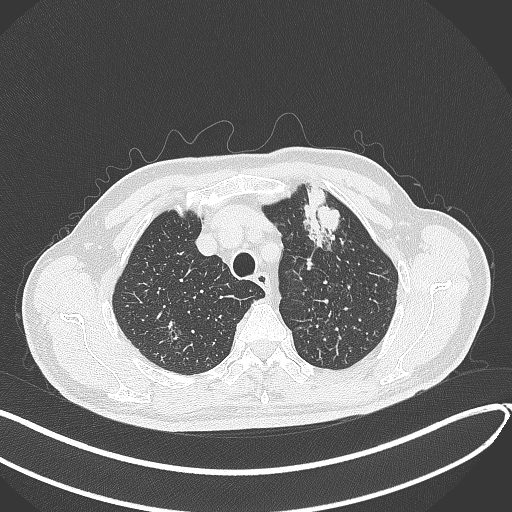
Chest CT, one axial slice; position 345 of 459 along the scan axis; 120 kVp; lung window (W 1500 / L -600 HU); 512 × 512 image matrix. Patient: male, 74 years. Case-level facts recorded for this patient, not image findings: clinical TNM (as recorded): T2b N0 M1c.
Outlined on this slice (rectangle marked by the reading radiologist):
- lung tumour (recorded histology: adenocarcinoma): box from (x=298, y=184) to (x=346, y=254) px